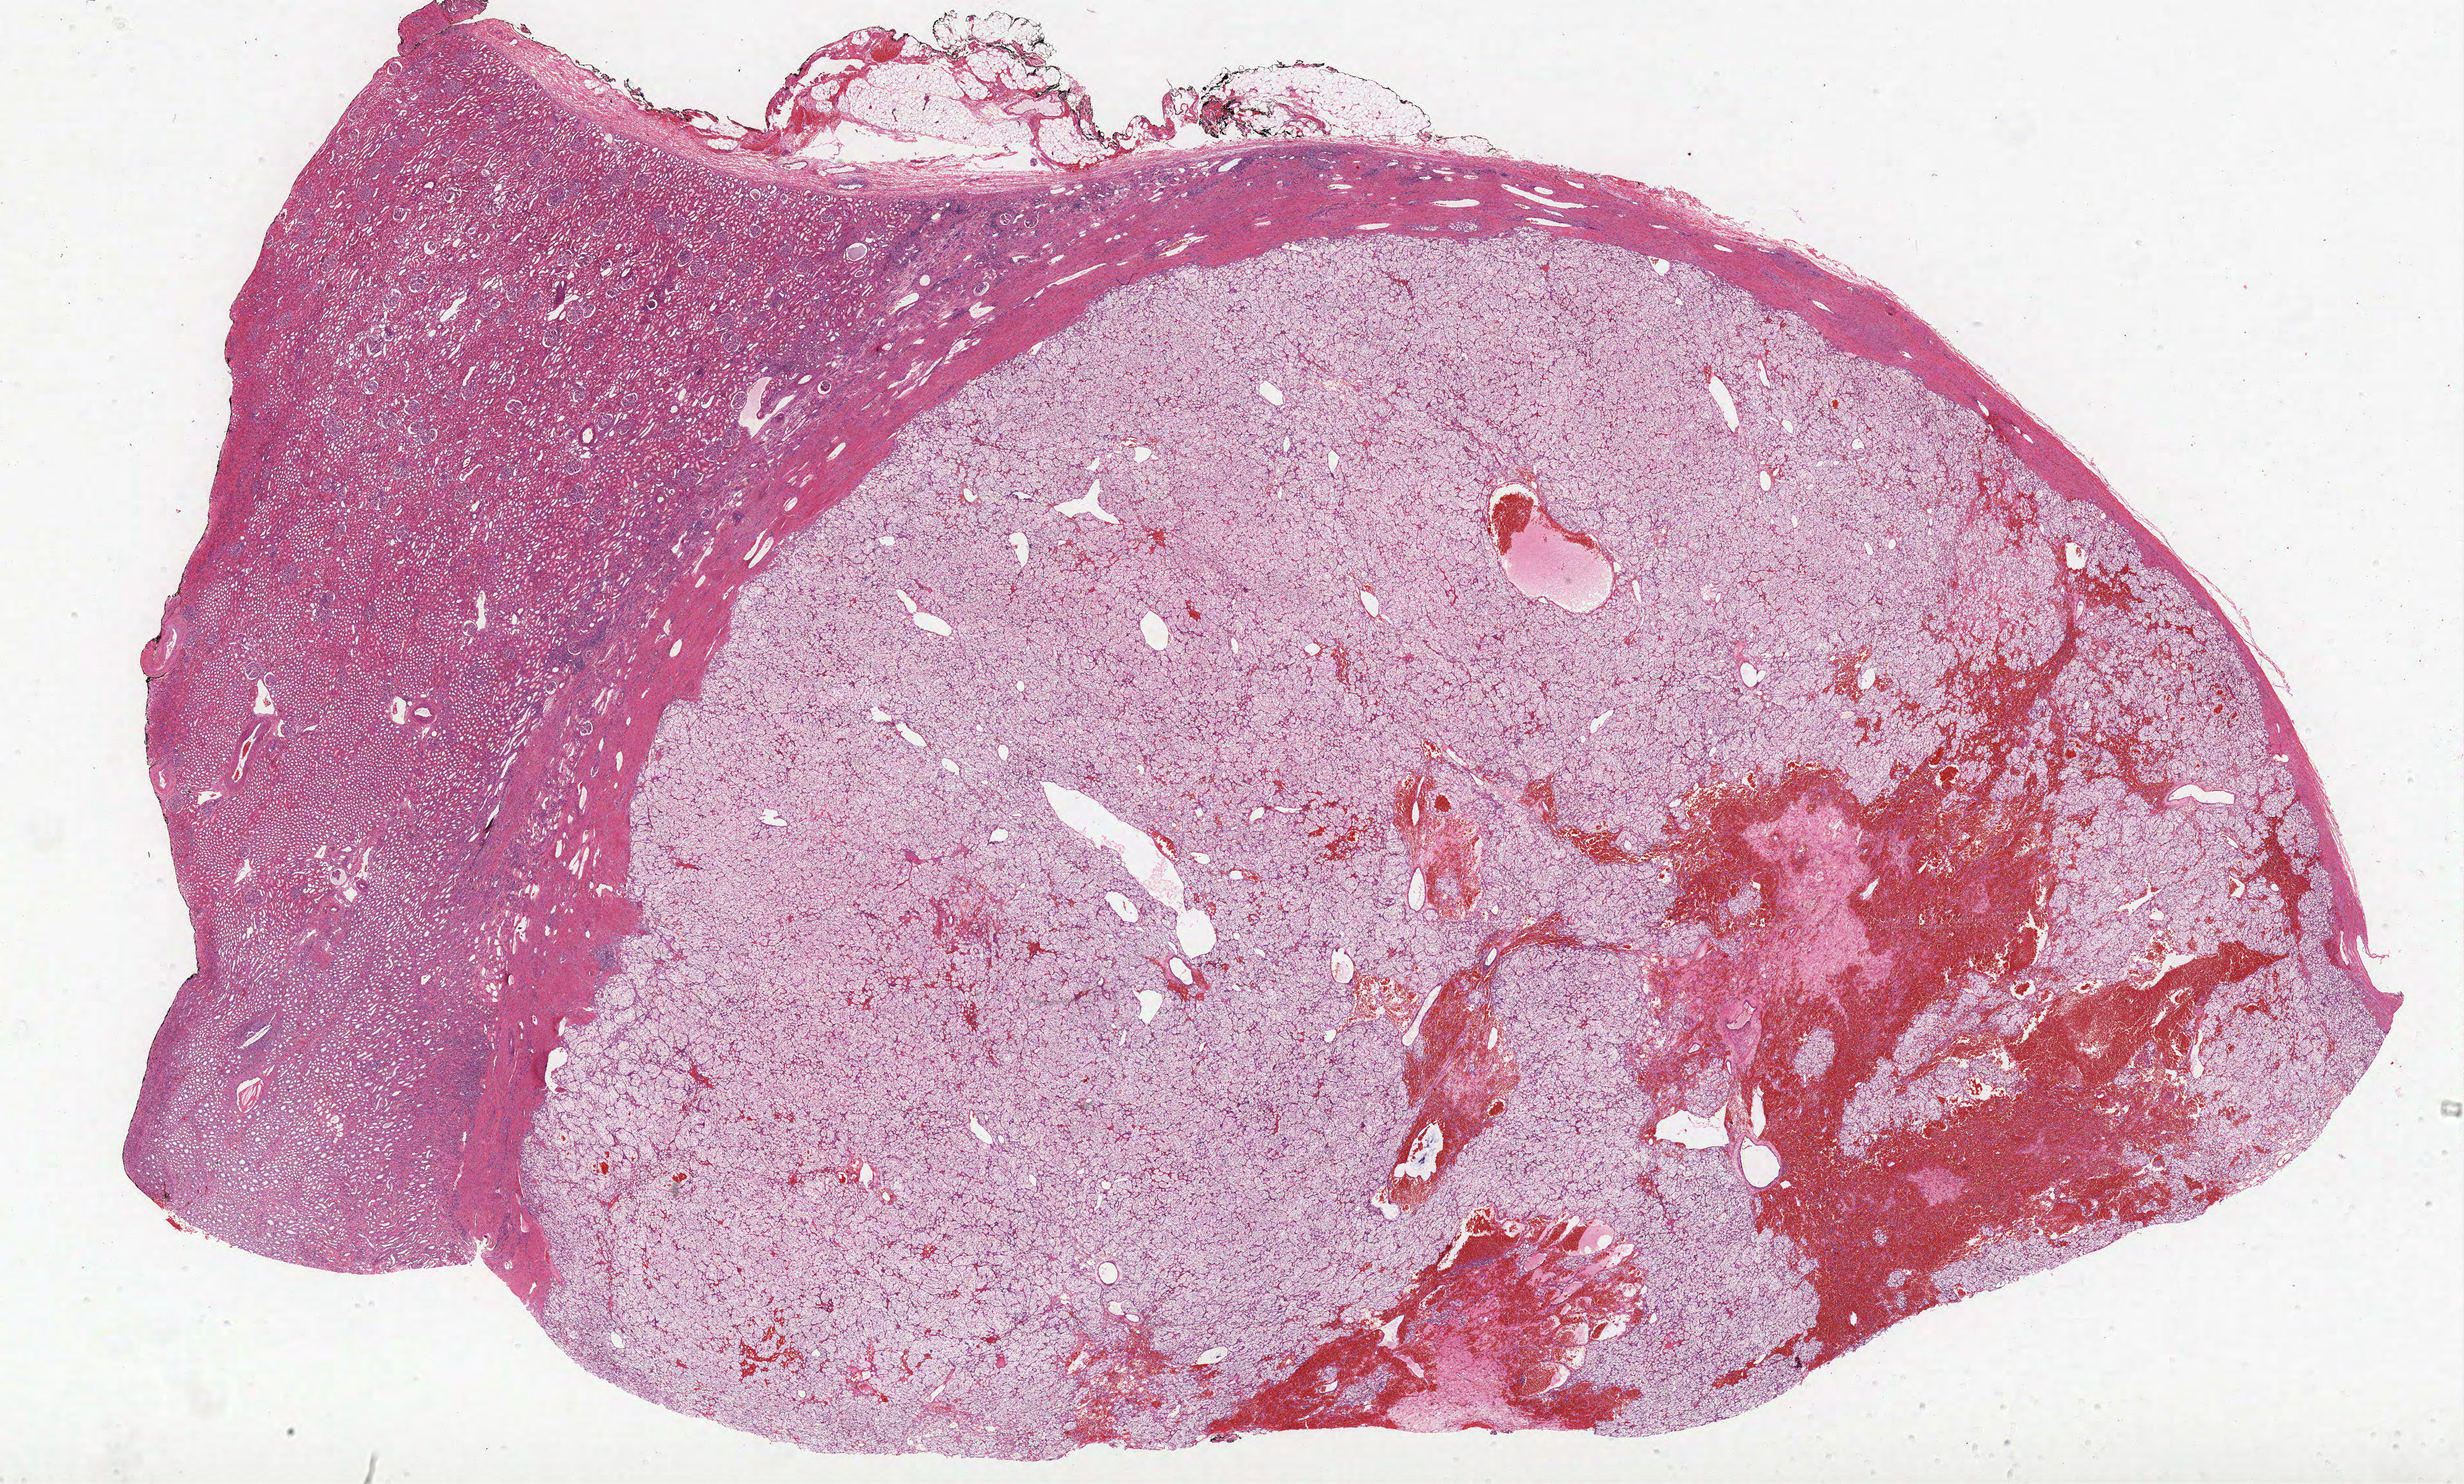
Digitized H&E tissue section (whole slide), shown as a low-resolution overview of the whole scanned area (about 30.2 x 18.2 mm), formalin-fixed paraffin-embedded (FFPE) diagnostic section, primary tumour sample from the kidney. Male, age 39 years at initial diagnosis.
Diagnosis: Clear cell adenocarcinoma, NOS.